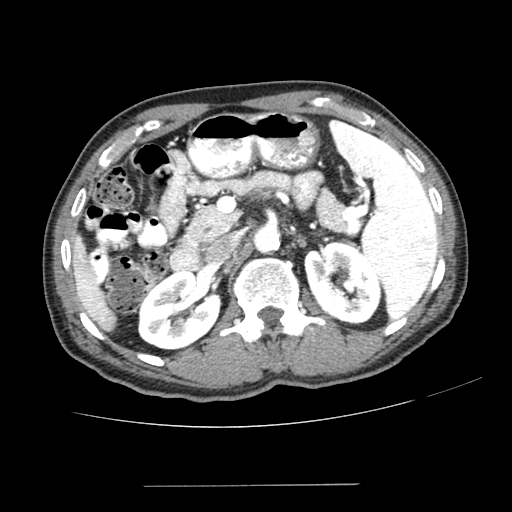
Contrast-enhanced abdominal CT (liver protocol), one axial slice; slice 137 of 187 in the series (ordered by position); 100 kVp; one of 2 acquisitions stored at this slice position; soft-tissue window (W 400 / L 40 HU); 2.5 mm slice thickness; 512 × 512 image matrix, field of view 360 × 360 mm. From the clinical record (not read from this slice): diagnosis: hepatocellular carcinoma (patient treated with transarterial chemoembolisation; whether this scan precedes or follows treatment is not stated here); TNM stage (as recorded): Stage-I; Child-Pugh class: A; tumour nodularity: uninodular; tumour size: 1.6 cm.
Annotated regions visible in this slice (semi-automatic segmentation, software-assisted and operator-edited):
- liver parenchyma outside the tumour (the mass and vessels are separate outlines, so this box may not span the whole liver): bounding box (x1, y1, x2, y2) in pixels: (72, 235, 116, 330)
- liver vessels: (79, 285, 100, 307)